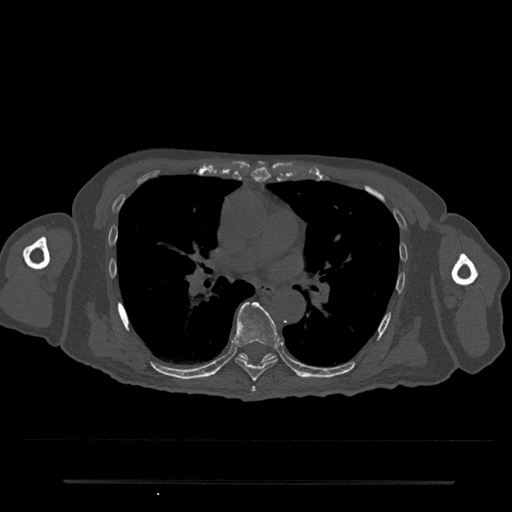
CT including the spine, one axial slice; slice 464 of 797 in the series (ordered by position); bone window (W 1800 / L 400 HU); 0.5 mm slice thickness; 512 × 512 image matrix, field of view 427 × 427 mm. Male patient, age 74 years. Case-level facts recorded for this patient, not image findings: primary cancer: prostate.
Annotated regions visible in this slice (semi-automatically segmented with operator editing):
- T6 vertebra: bounding box [x1, y1, x2, y2] px = [251, 386, 256, 392]
- T7 vertebra: [233, 302, 280, 382]
- T8 vertebra: [239, 353, 276, 362]